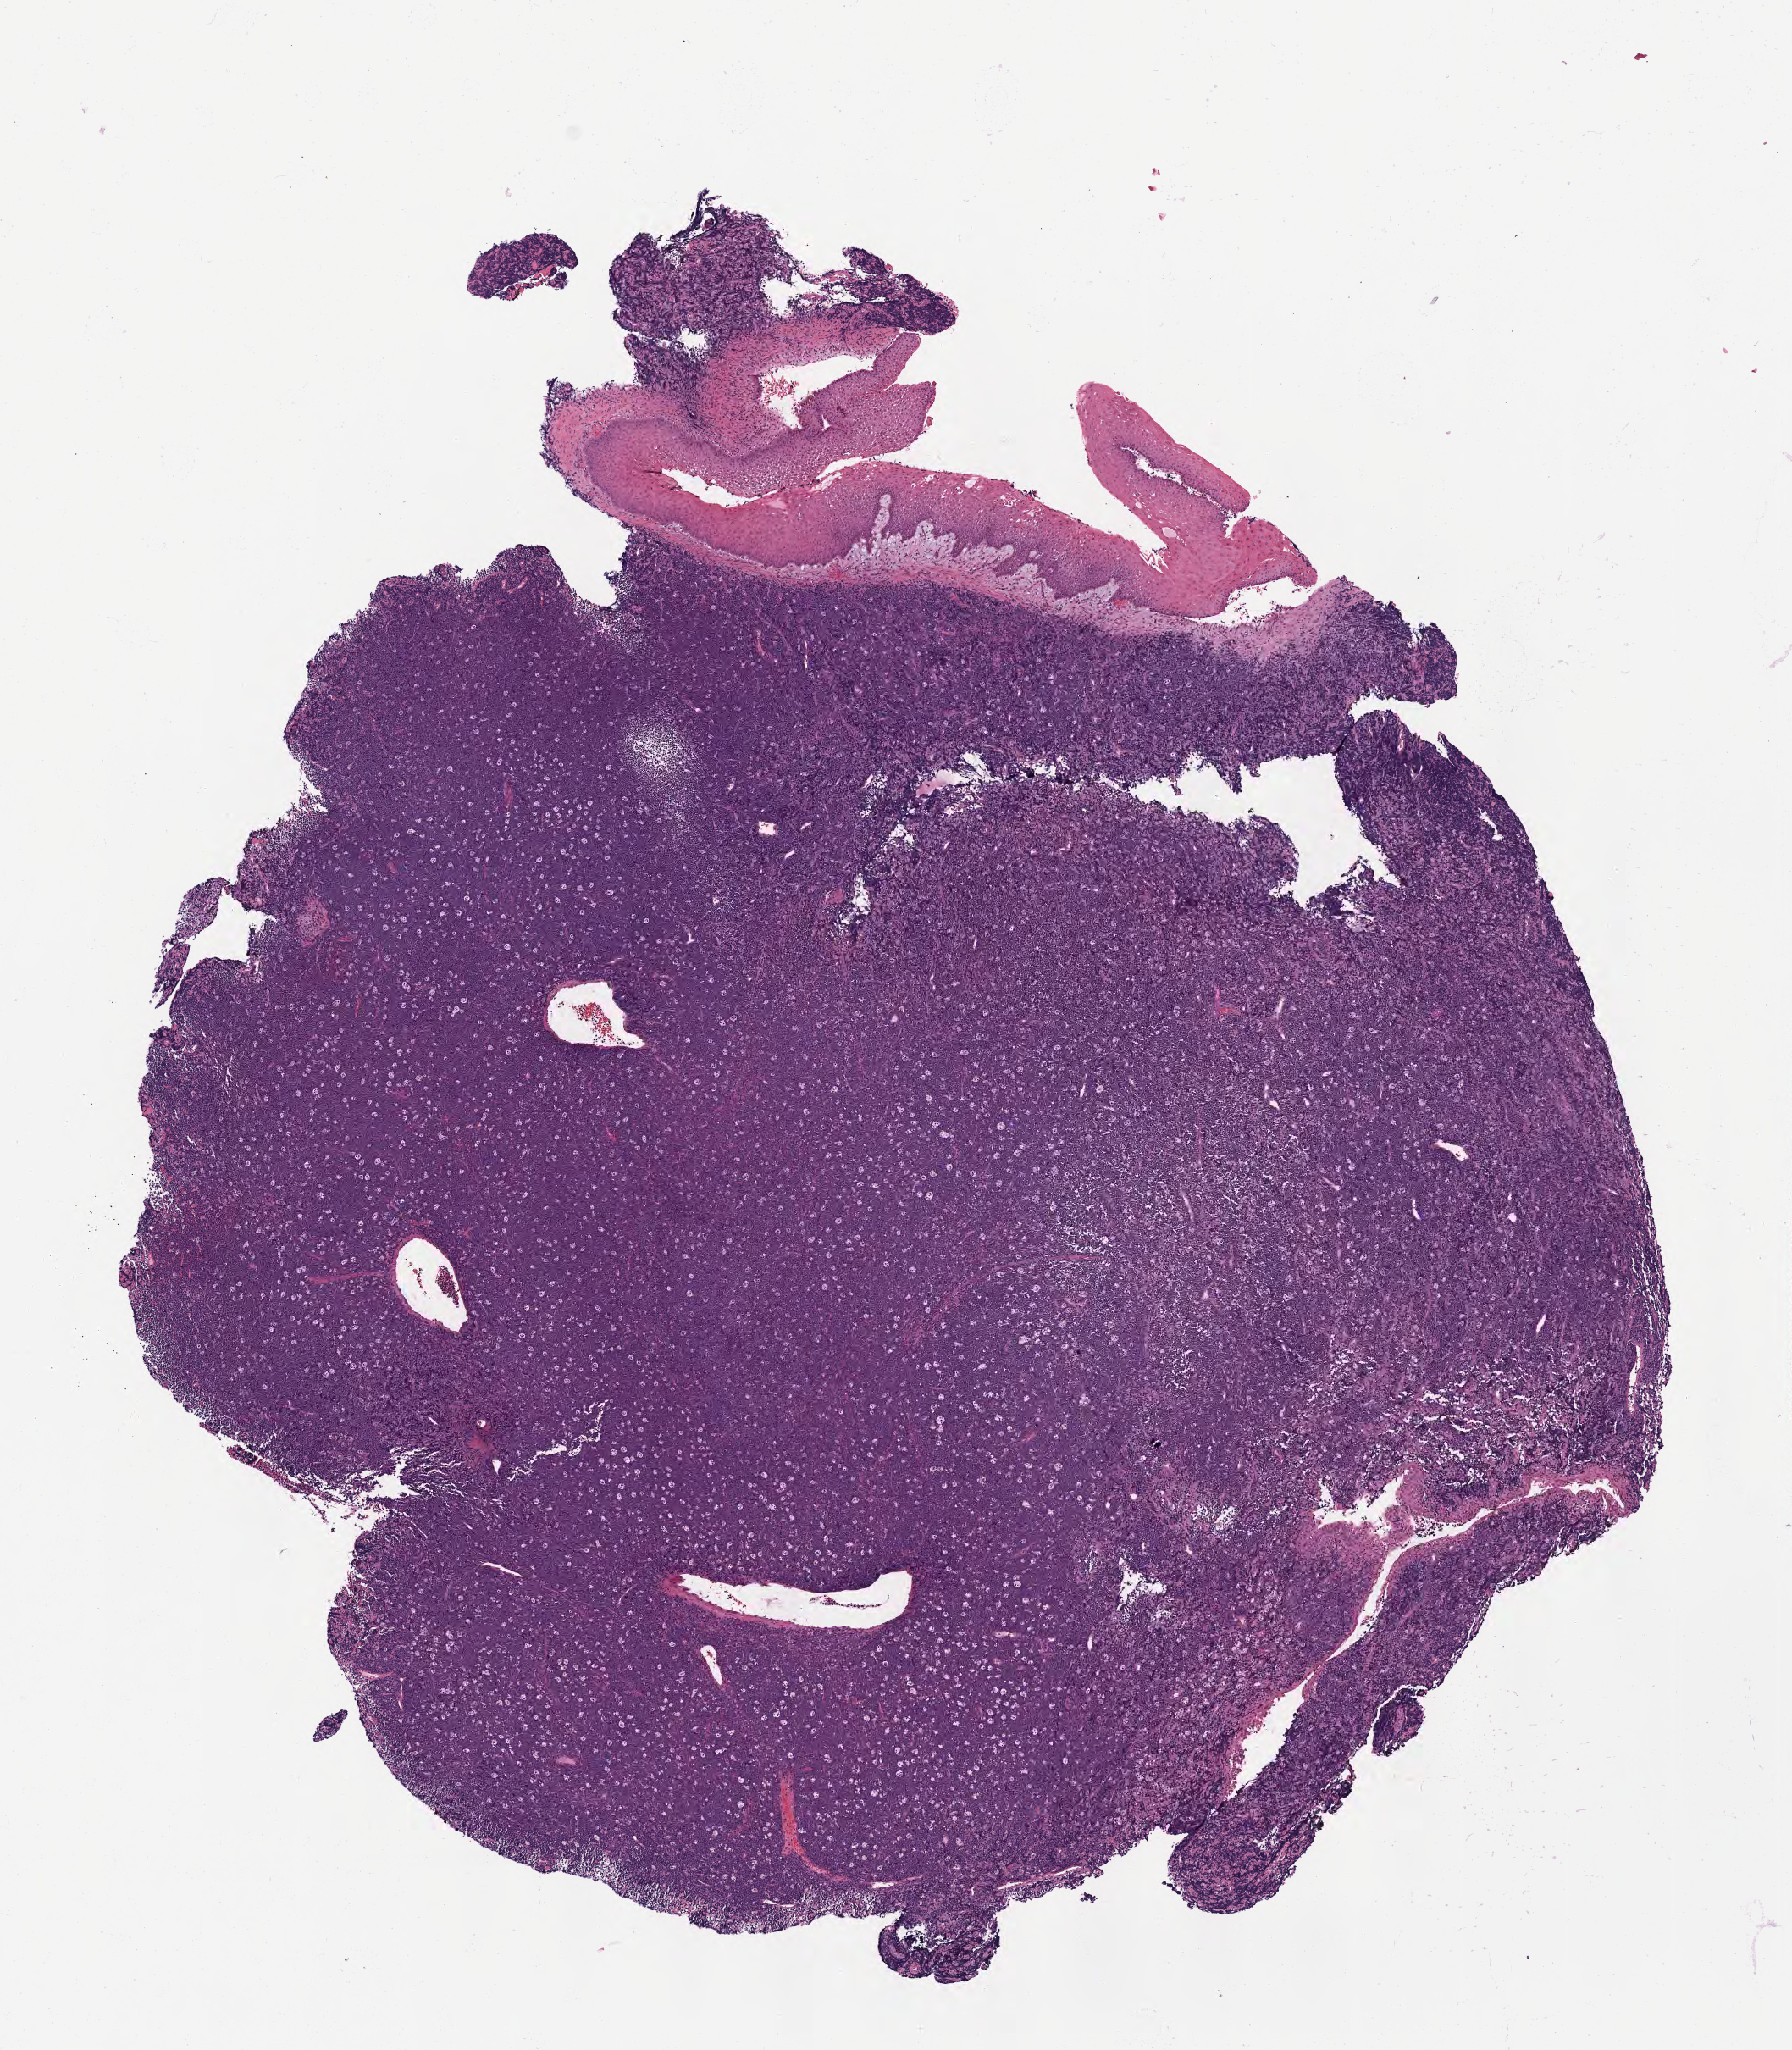
H&E whole-slide image — whole scanned area (about 8.6 x 9.8 mm) shown as a low-resolution overview. FFPE section. Specimen: primary tumor. Anatomic site: buccal mucosa. Female, age 7 years at initial diagnosis. Slide review estimates, as recorded: tumor cells 90%, tumor nuclei 95%, stromal cells 5%, necrosis 5%, normal cells 0%. Inflammatory infiltration, as recorded: lymphocyte infiltration 40%, monocyte infiltration 30%, neutrophil infiltration 5%.
* section: top of the tissue portion
* diagnosis: Burkitt lymphoma, NOS
* Ann Arbor stage (patient): Stage III